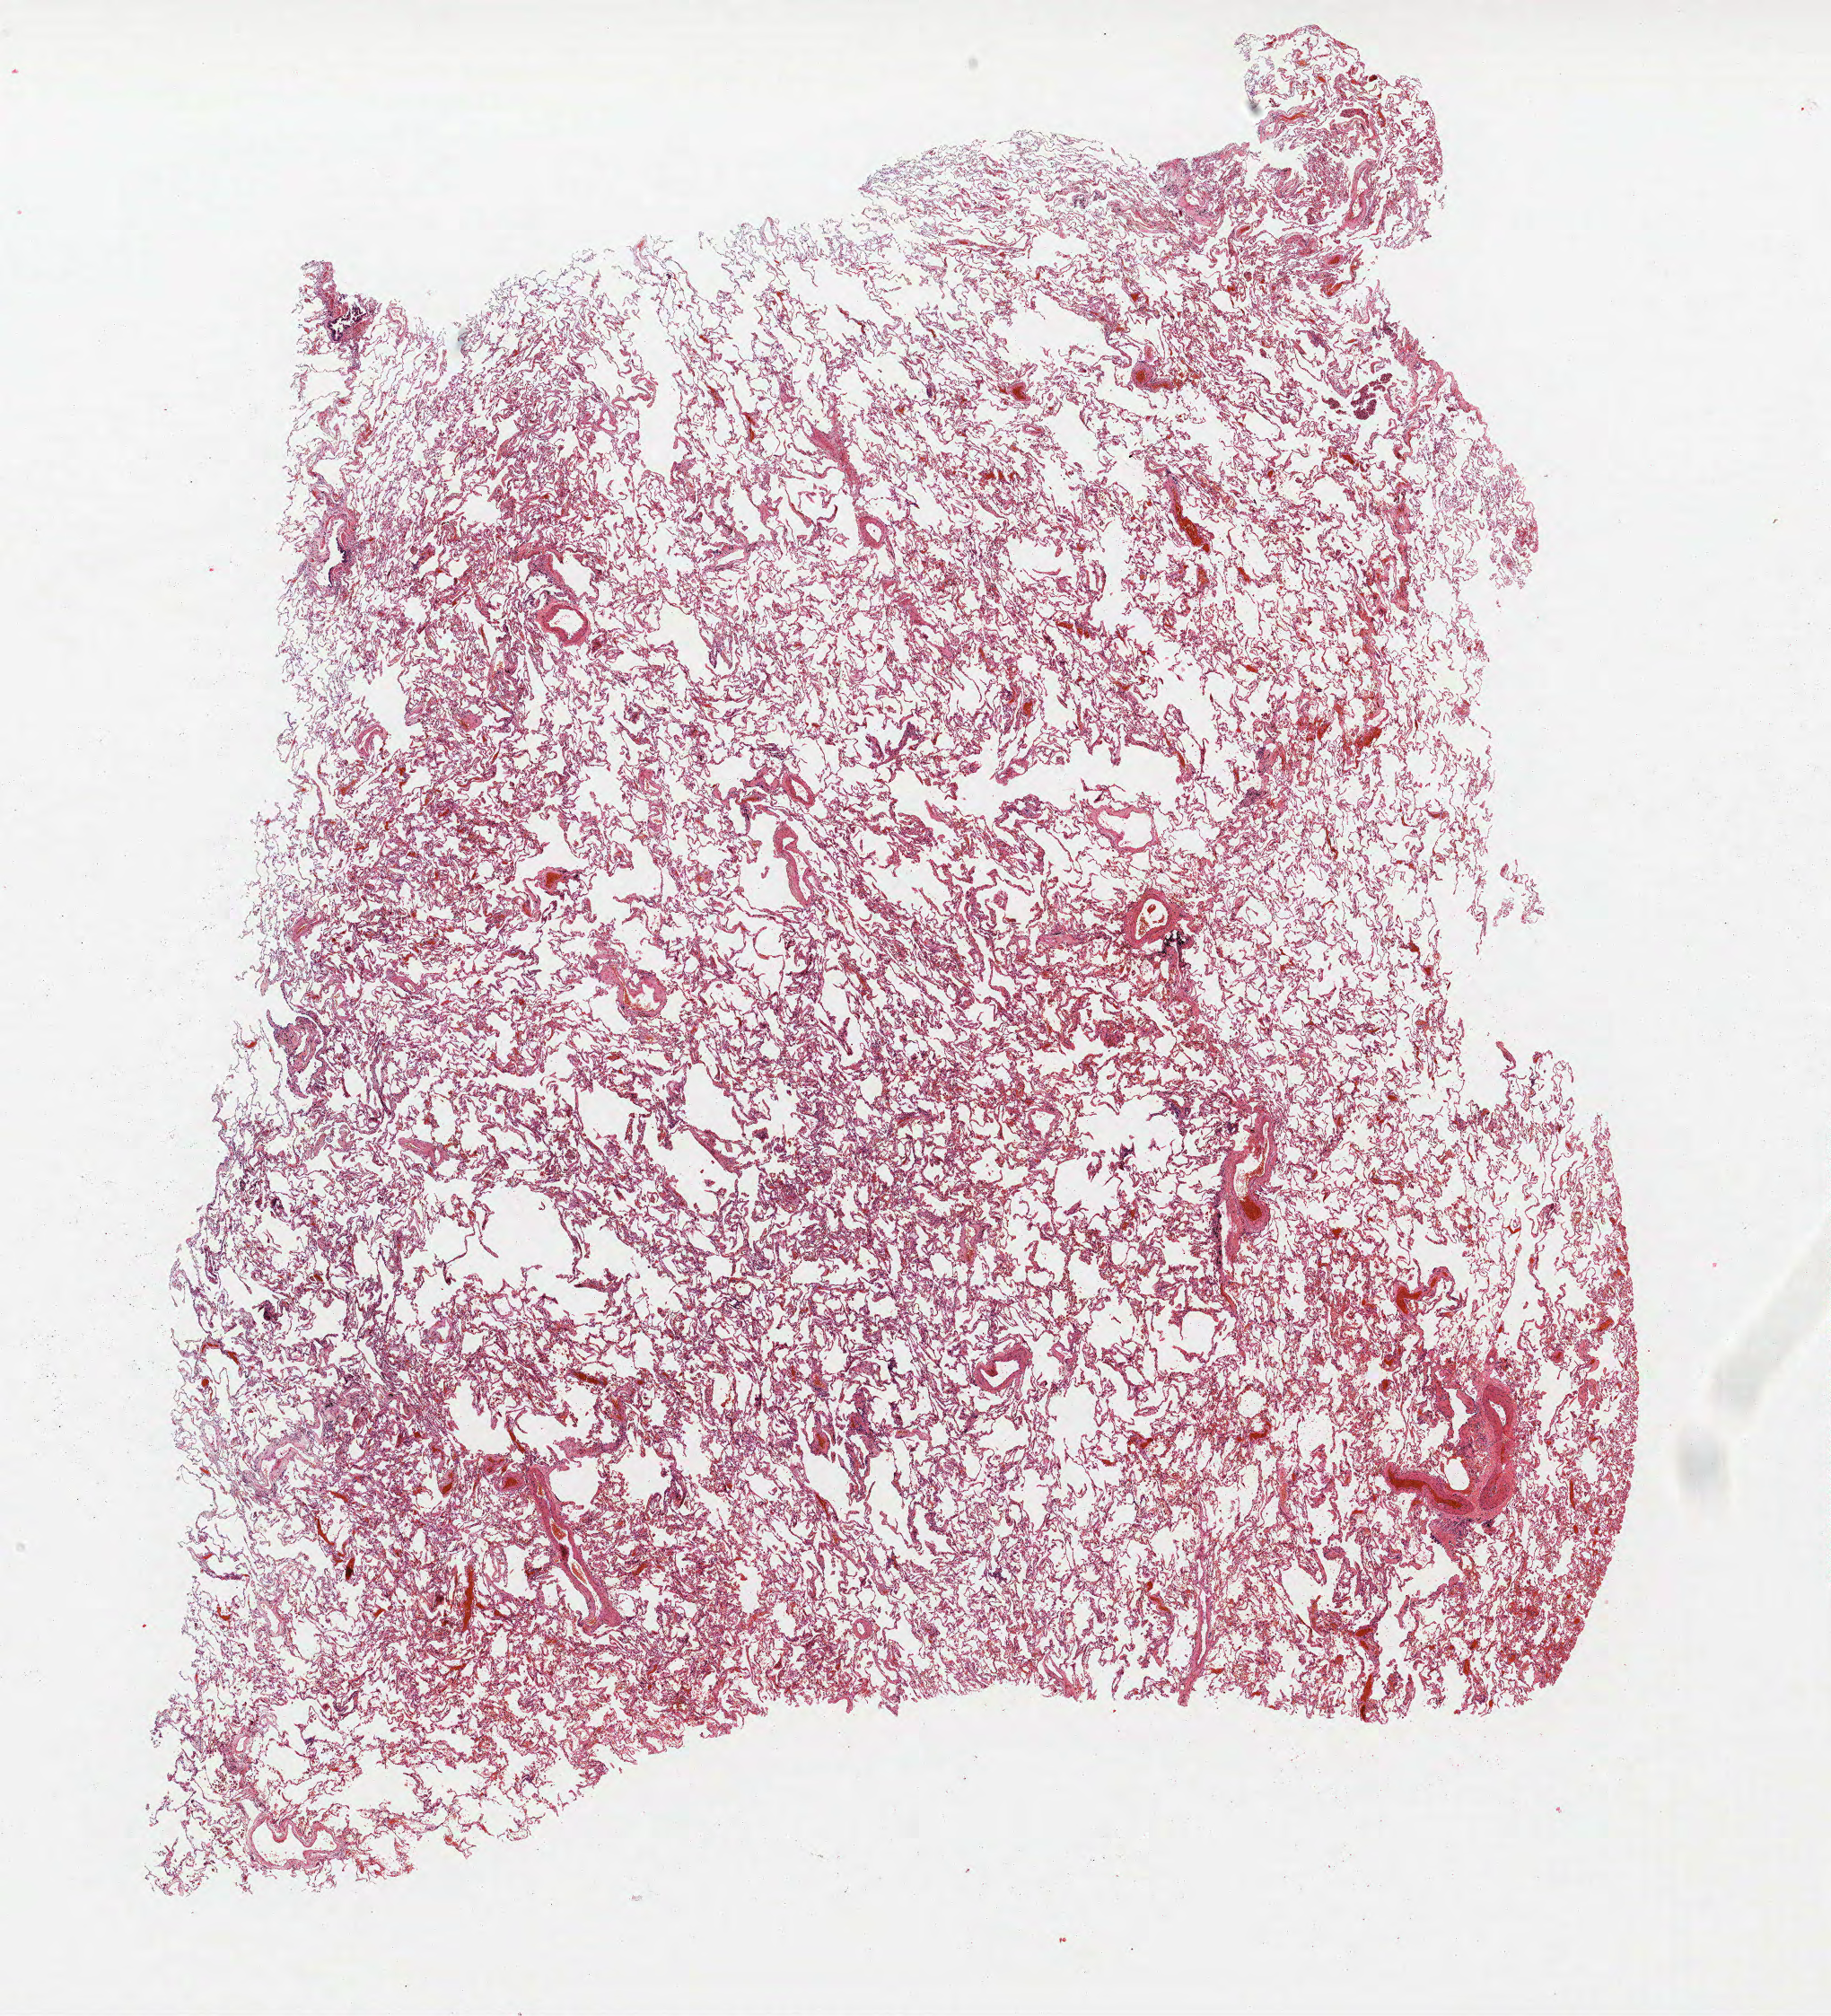
Hematoxylin and eosin (H&E) stained whole-slide image — shown as a low-resolution overview of the whole scanned area (about 16.3 x 18.0 mm, slide scanned at 40x); FFPE section; lung. Male patient, aged 68 at enrolment. Grade: well differentiated (G1).
- tumour size (pathology): 12 mm
- participant's lung-cancer diagnosis: Bronchiolo-alveolar adenocarcinoma, NOS
- stage (AJCC 6th edition): IA
- primary tumour location (clinical record): right lower lobe
- ICD-O-3 topography: lower lobe of lung (C34.3)